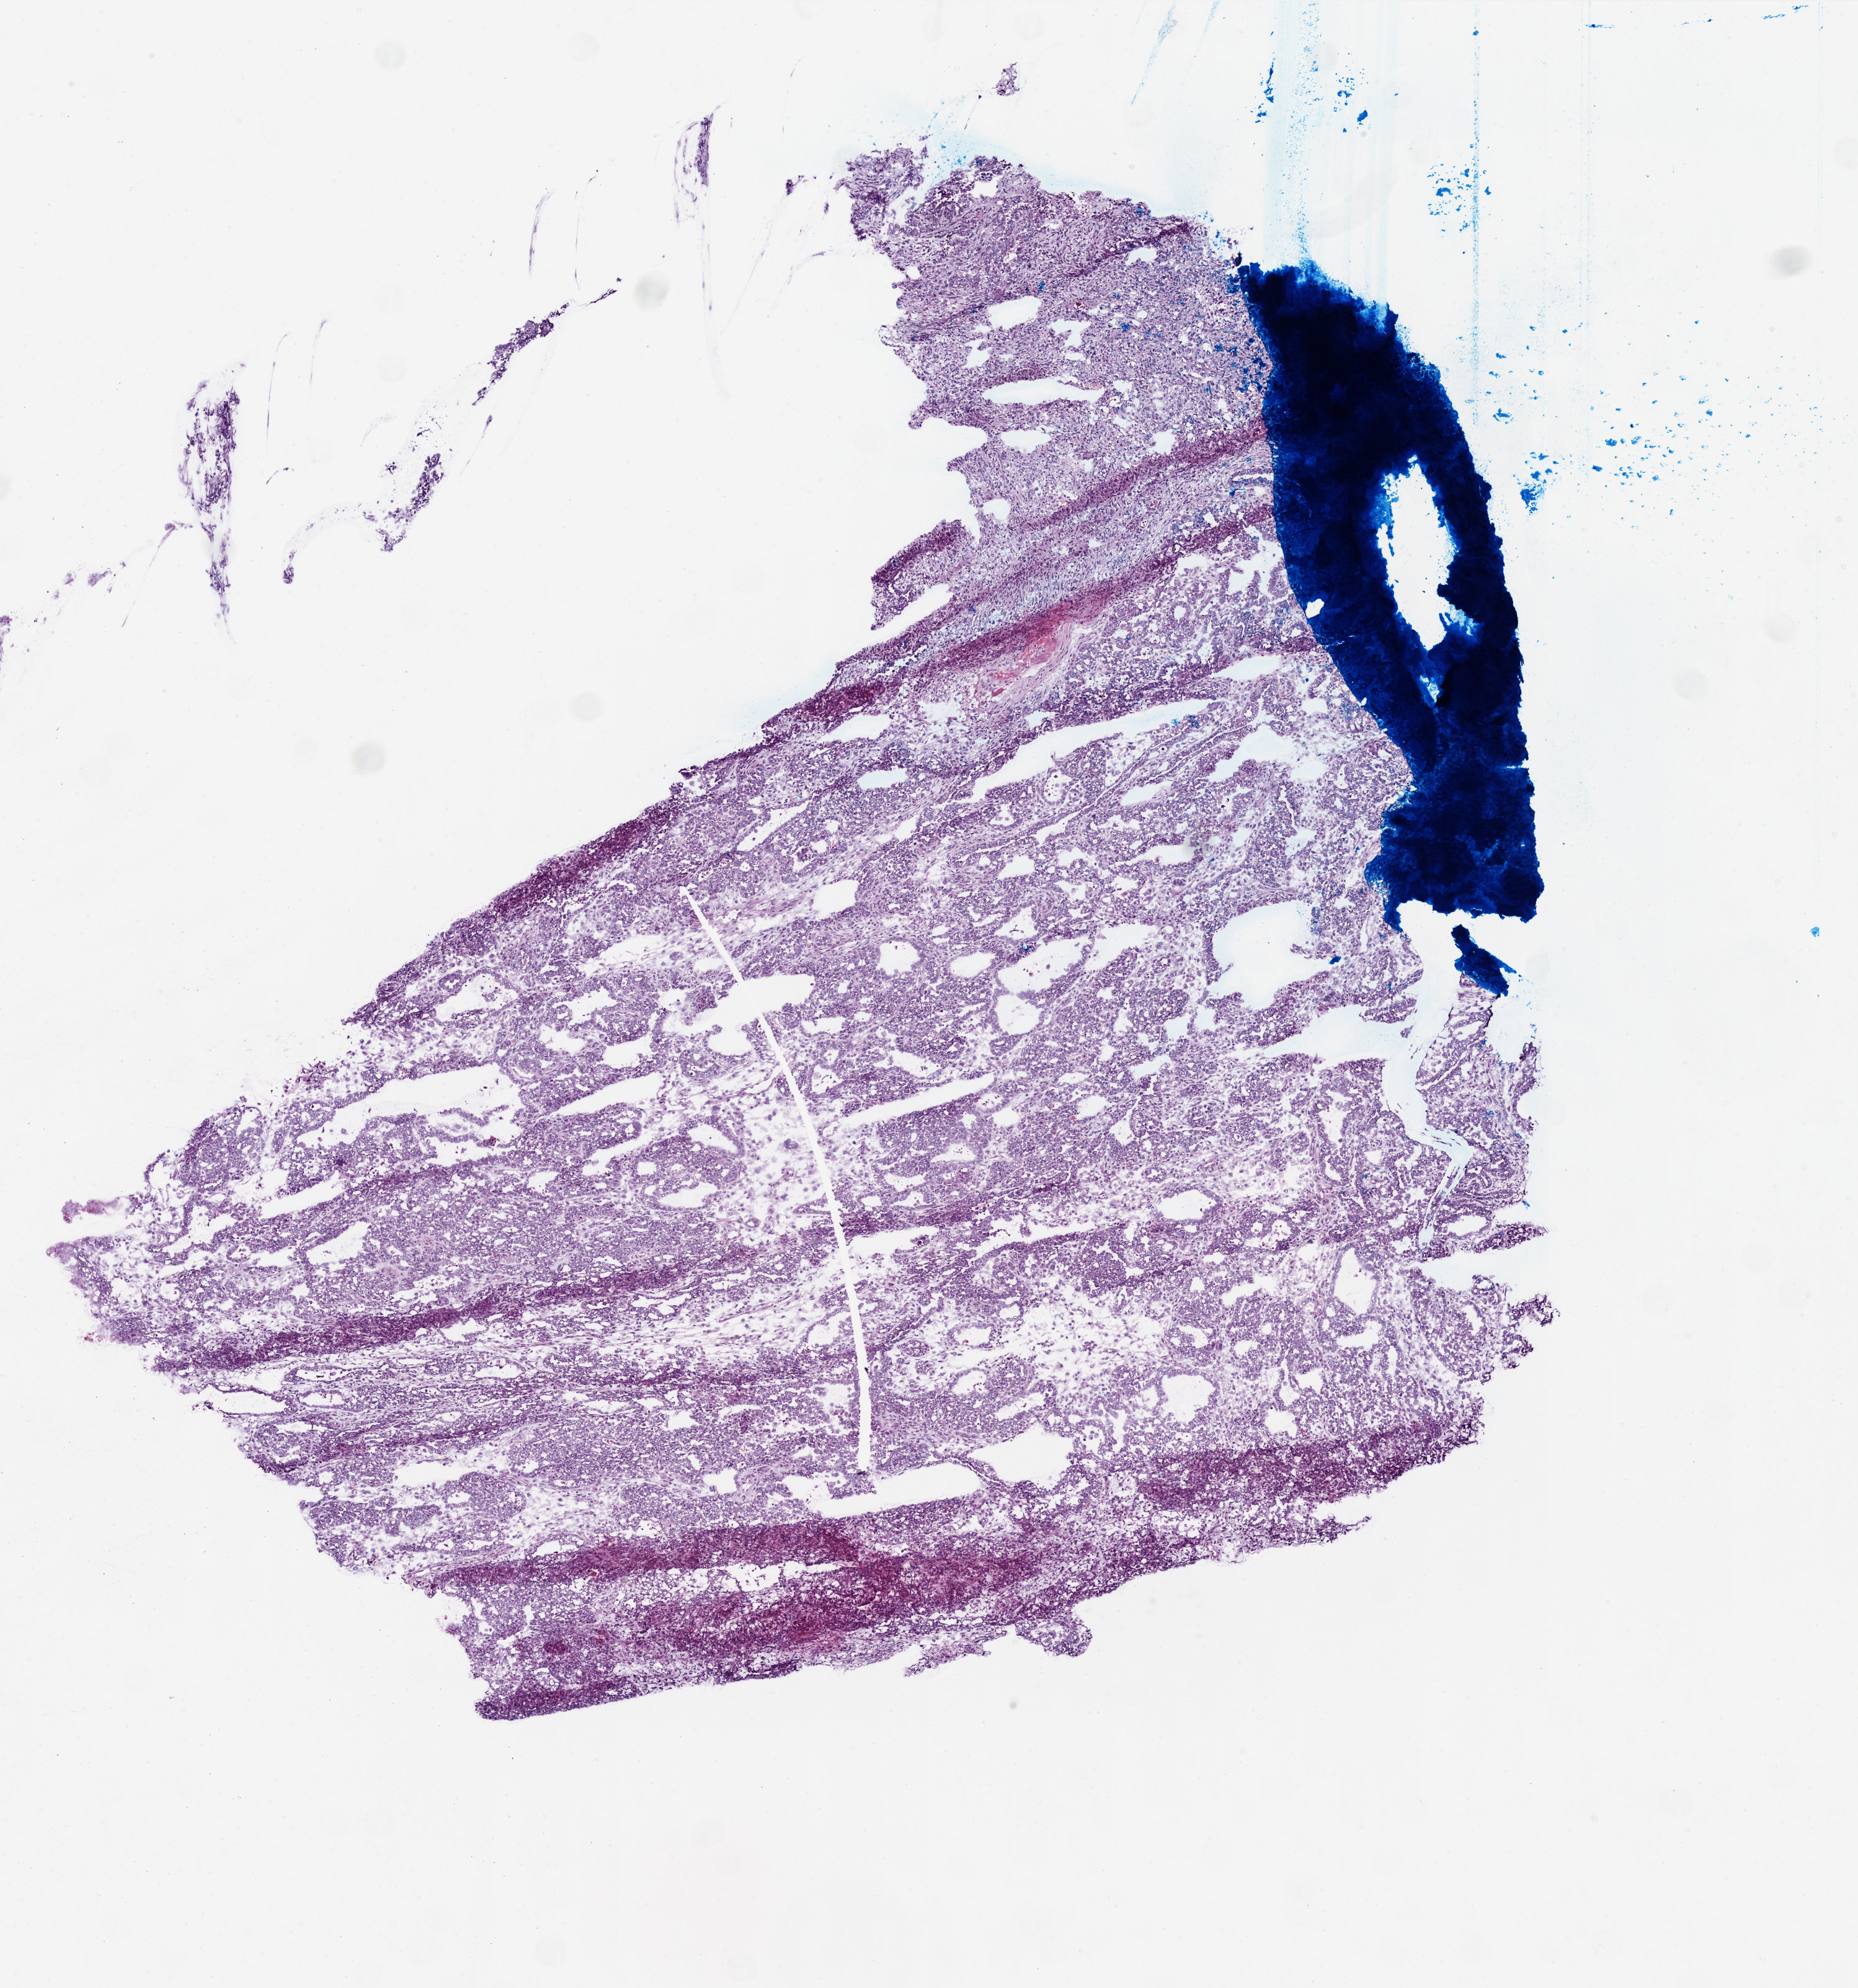
Whole-slide histology image, Hematoxylin and eosin (H&E) stained — shown as a low-resolution overview of the whole scanned area (about 6.0 x 6.4 mm, from a 20x scan), frozen section from the top of the tissue portion, ovary, primary tumour sample. Female, age 56 years at initial diagnosis. Histologic grade: G3 (poorly differentiated). Slide review estimates, as recorded: tumour cells 95%, tumour nuclei 98%, normal cells 0%, stromal cells 5%, necrosis 0%.
Histologic diagnosis: Serous cystadenocarcinoma, NOS. FIGO stage: IIIC. Laterality: left.